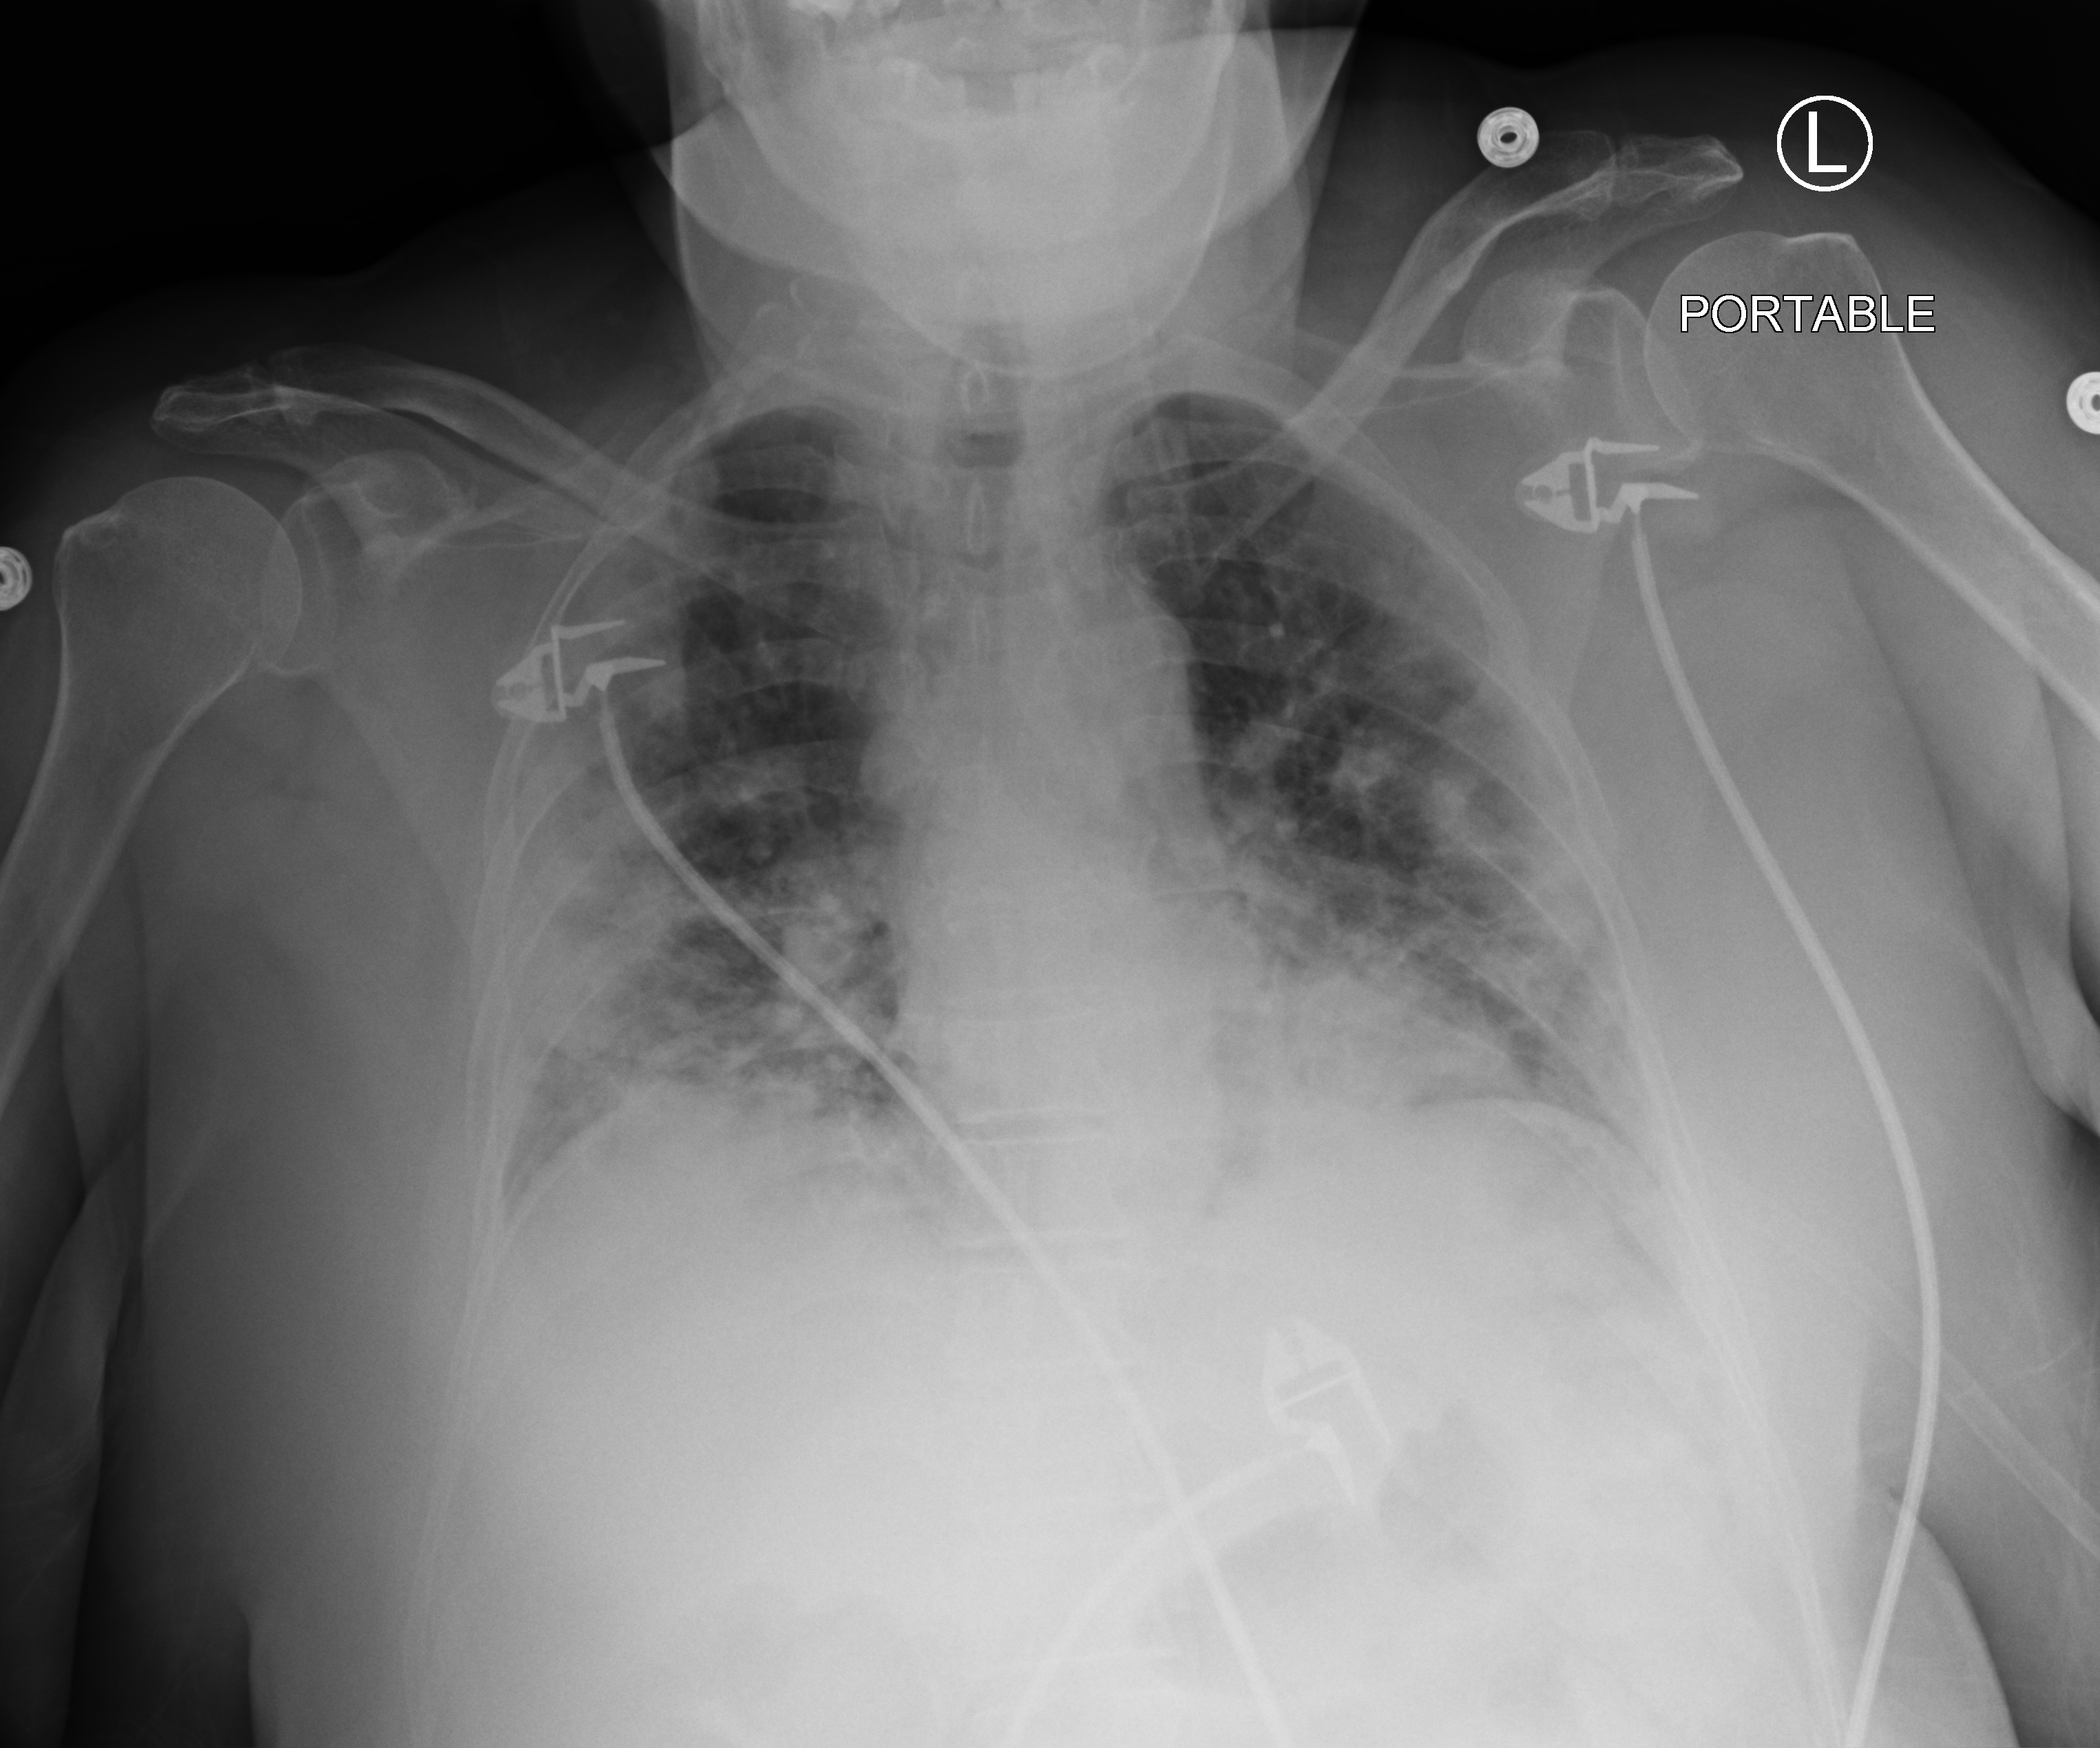
Chest X-ray (portable). Female patient hospitalised with COVID-19, age 60–74 years.
Admission-level facts for this patient (not findings on this image; timing relative to this image not recorded):
- smoking status (admission record): never
- length of hospital stay: 14 days
- hypertension (admission record): no